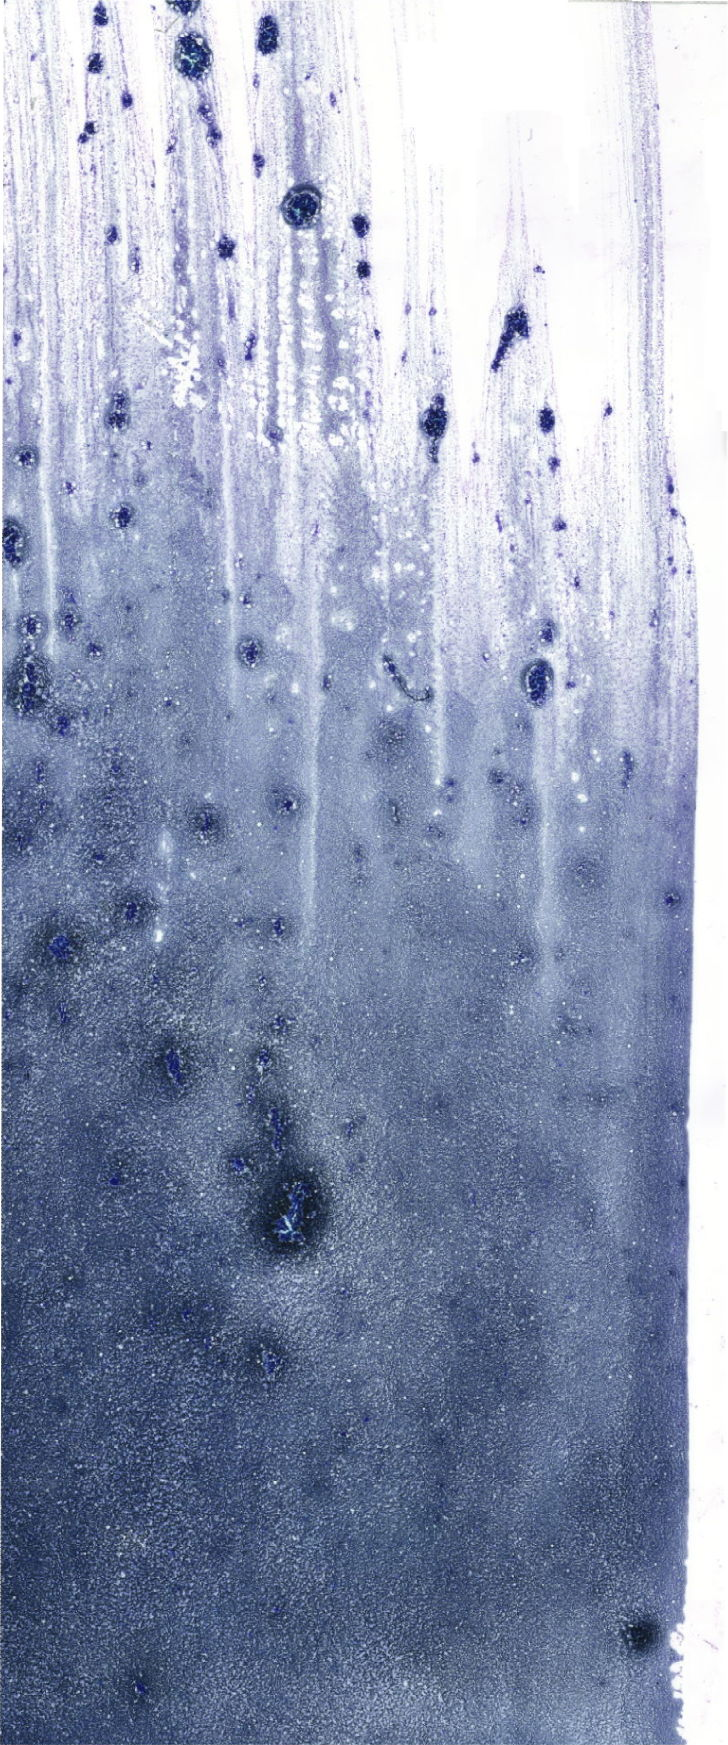
May-Grünwald–Giemsa-stained marrow aspirate smear (whole slide) — low-resolution overview of the scanned area, about 20.6 x 49.5 mm. Female patient.
- diagnosis: T Acute Lymphoblastic Leukemia